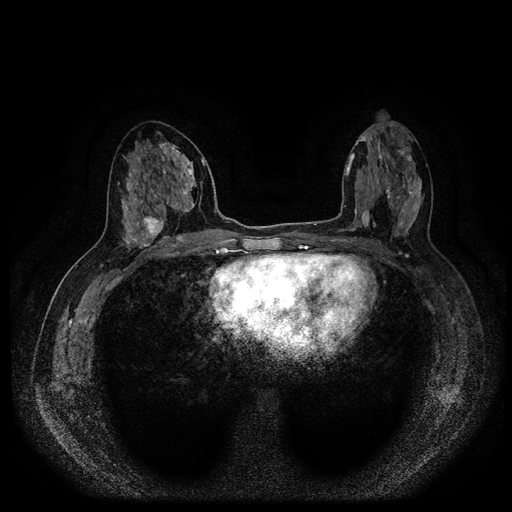
Breast MRI (dynamic contrast-enhanced, multi-phase), one axial slice. Slice 48 of 116 in the series (ordered by position). Dynamic contrast-enhanced series, time point 2 of 5 at this slice position (early post-contrast). 1.5 T. TE 2.6 ms, TR 5.4 ms. 2 mm slice thickness. 512 × 512 image matrix, field of view 340 × 340 mm. Patient: female, 48 years.
Structures marked on this image (semi-automatic segmentation, software-assisted and operator-edited):
- breast lesion (labelled 'tumour' in the annotation; benign lesions carry a separate 'benign' label): bounding box <142,215,167,242> (left, top, right, bottom; pixels)